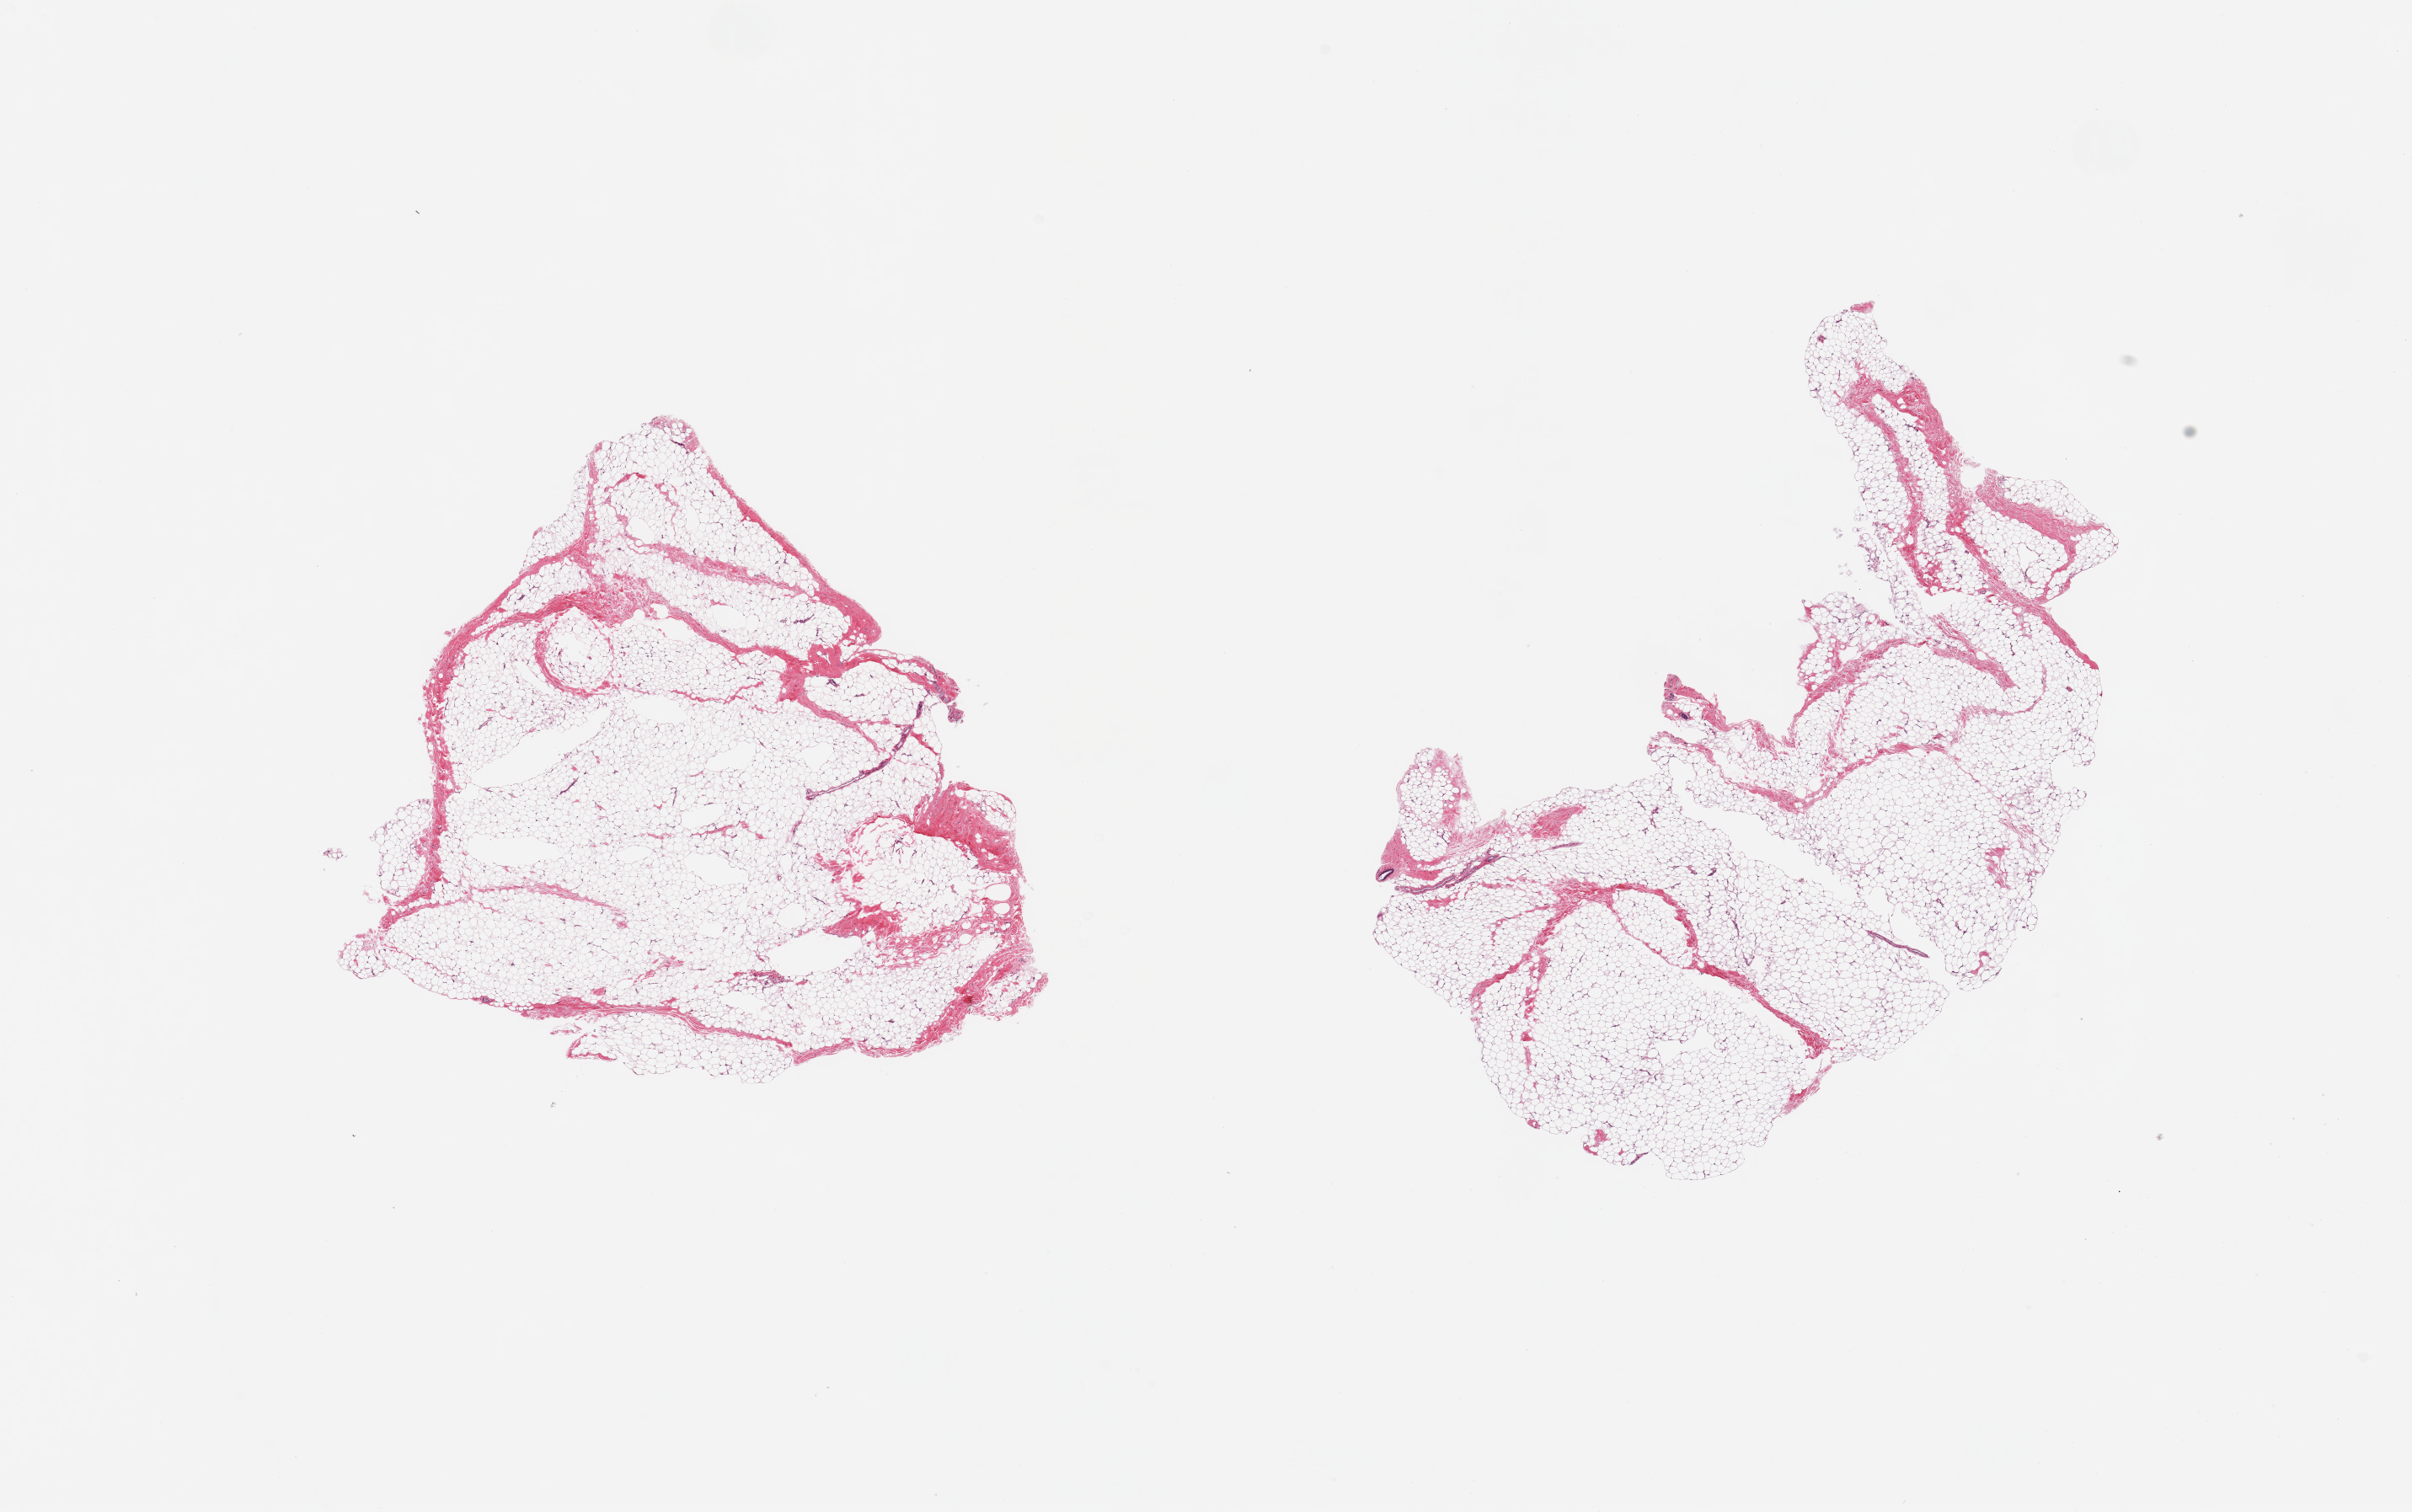
Digitized H&E-stained section — low-resolution overview of the scanned area, about 22.6 x 14.2 mm, PAXgene-fixed paraffin-embedded (PFPE) section, sampled site (target tissue): breast, donor tissue sample. Donor sex: male.
Review note (as recorded): 2 pieces; adipose tissue with 1 duct; 5% fibrous content.